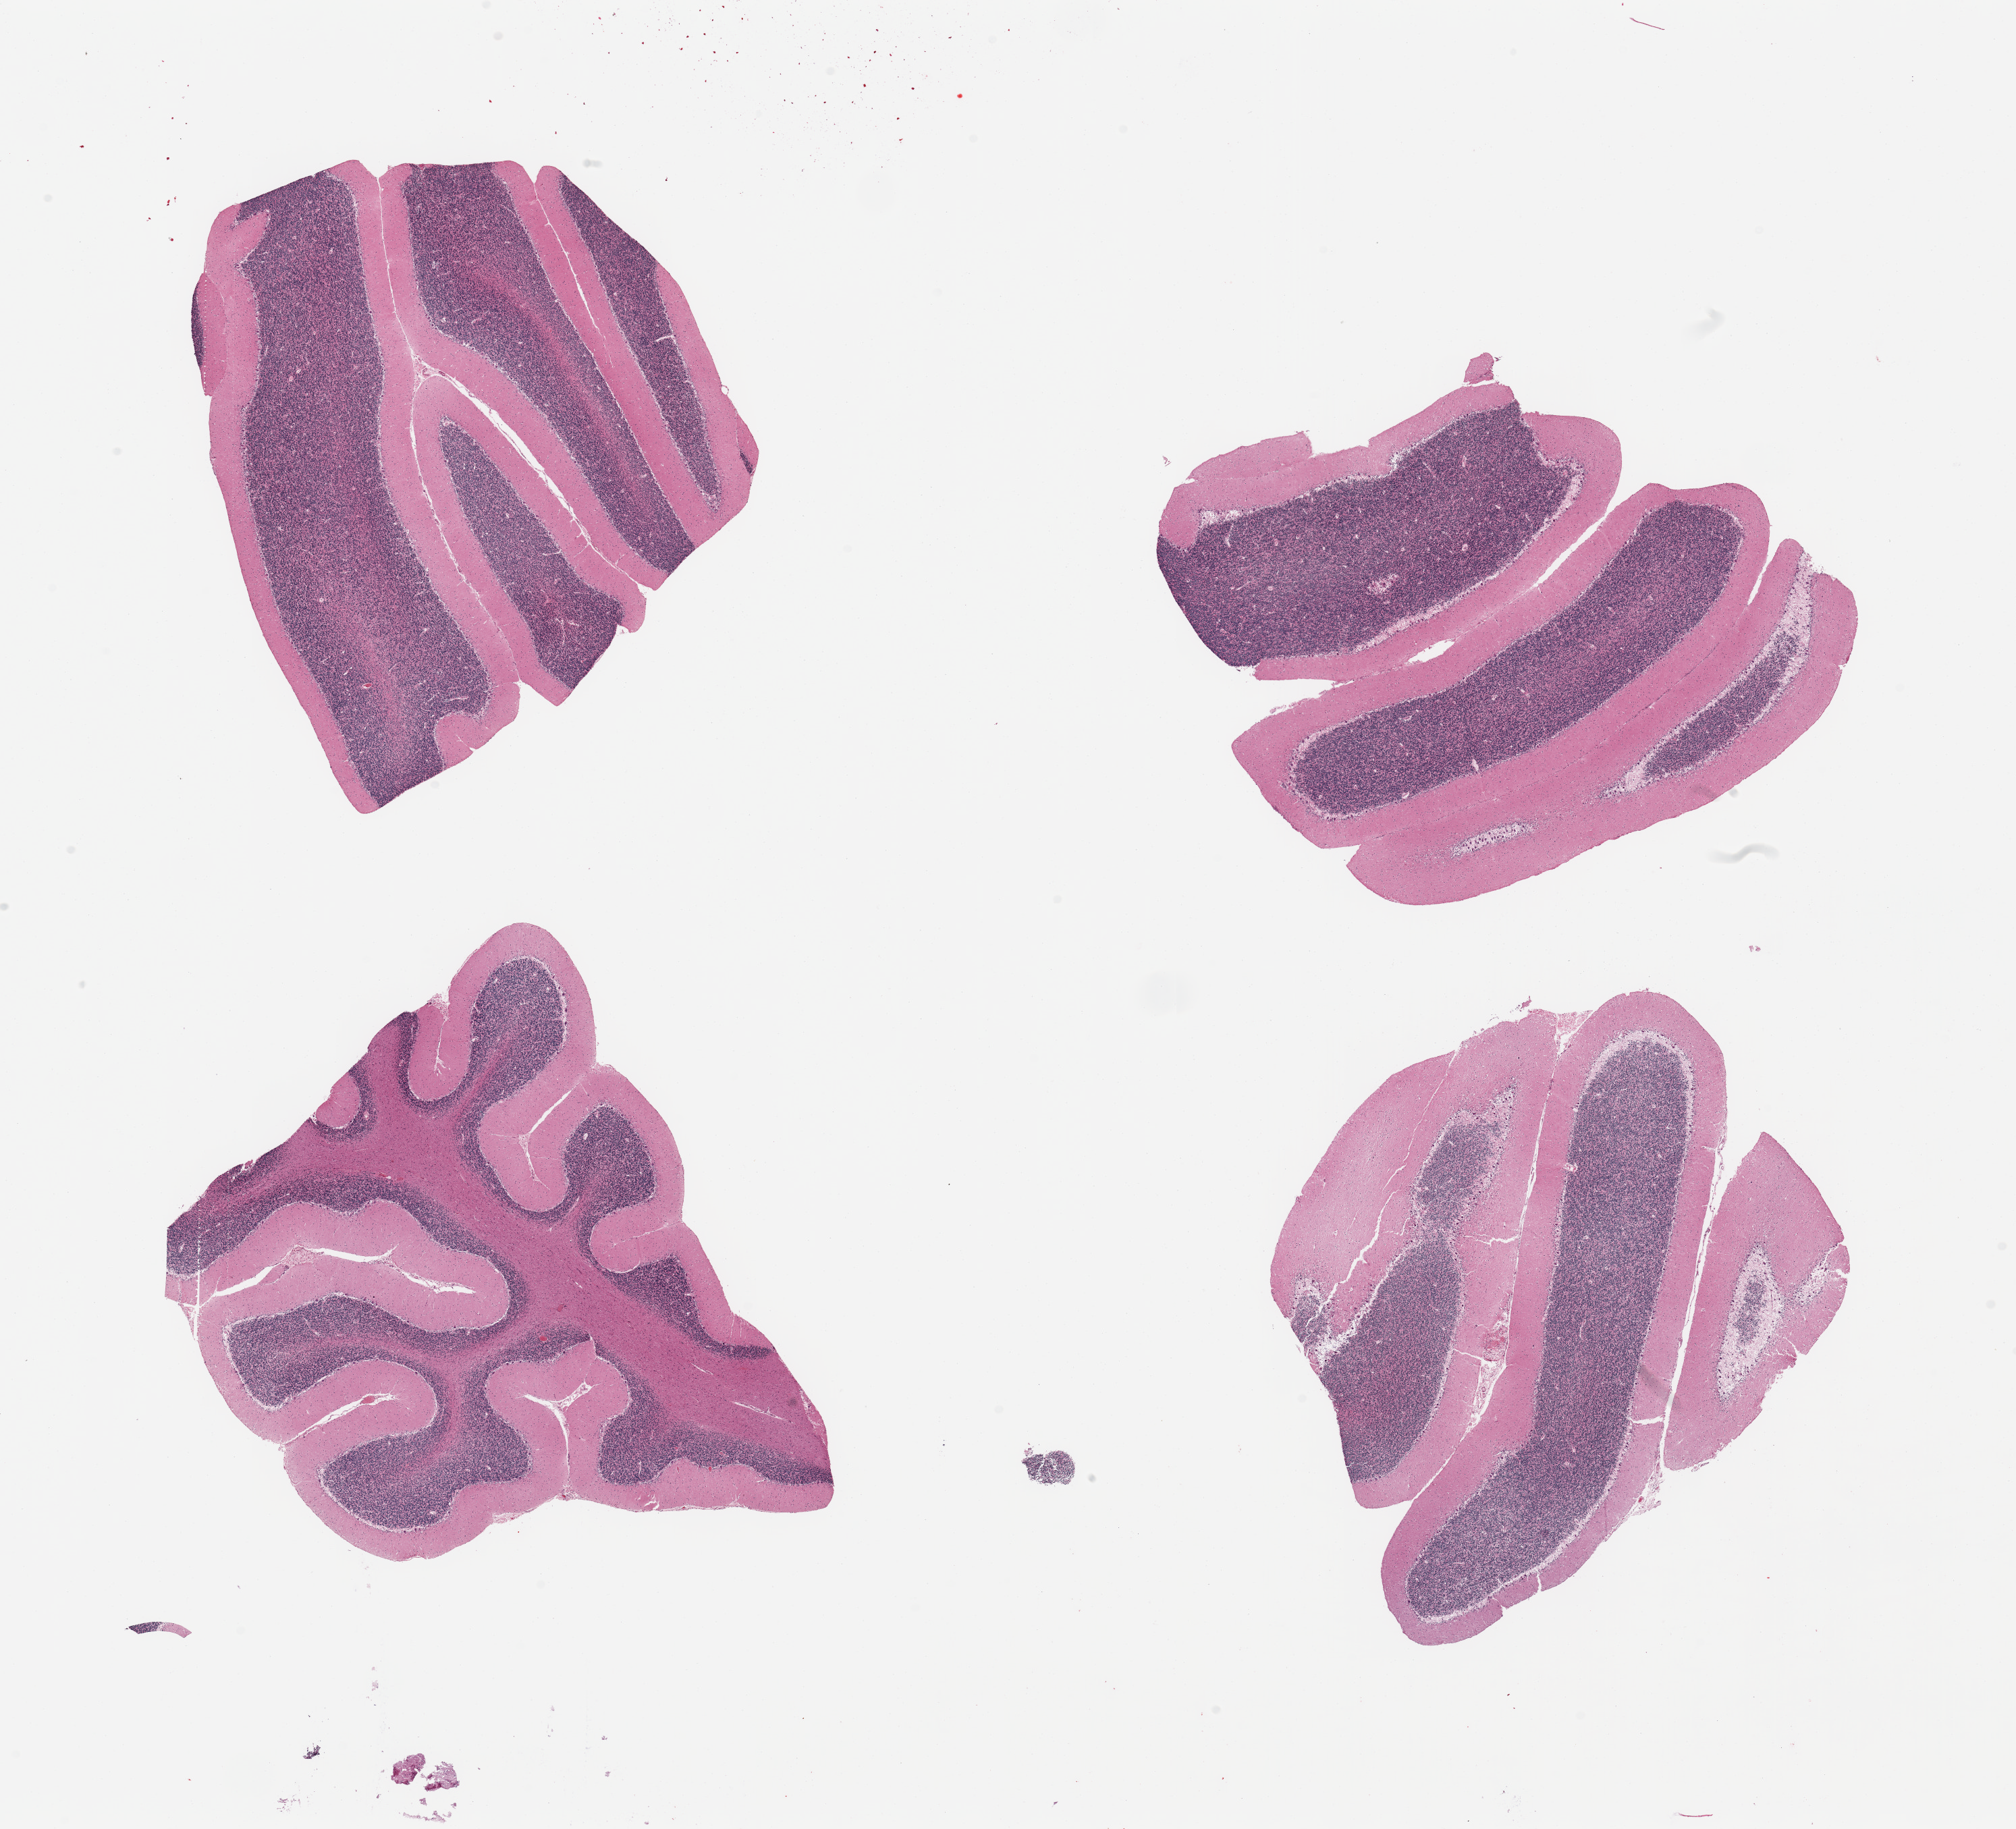
Digitized haematoxylin and eosin-stained section — whole scanned area (about 23.6 x 21.4 mm) shown as a low-resolution overview; PAXgene-fixed paraffin-embedded (PFPE) section; sampled site (target tissue): cerebellum; tissue donor sample. Male donor.
Reviewer comment on this tissue sample: 4 pieces.